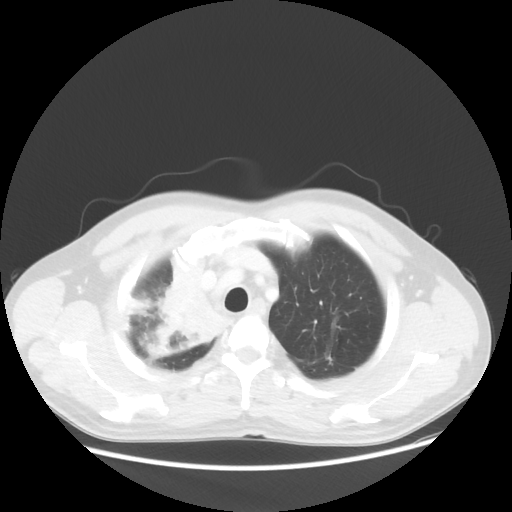
Chest CT, one axial slice. Slice 45 of 56 in the series (ordered by position). Reconstruction kernel STANDARD. 100 kVp. Lung window (W 1500 / L -600 HU). 5 mm slice thickness. 512 × 512 image matrix. Patient: male, 60 years. From the clinical record (not read from this slice): clinical TNM (as recorded): T2a N1 M0.
Outlined on this slice (bounding box drawn by a radiologist):
- lung tumour (recorded histology: squamous cell carcinoma): bounding box <122,241,229,369> (left, top, right, bottom; pixels)